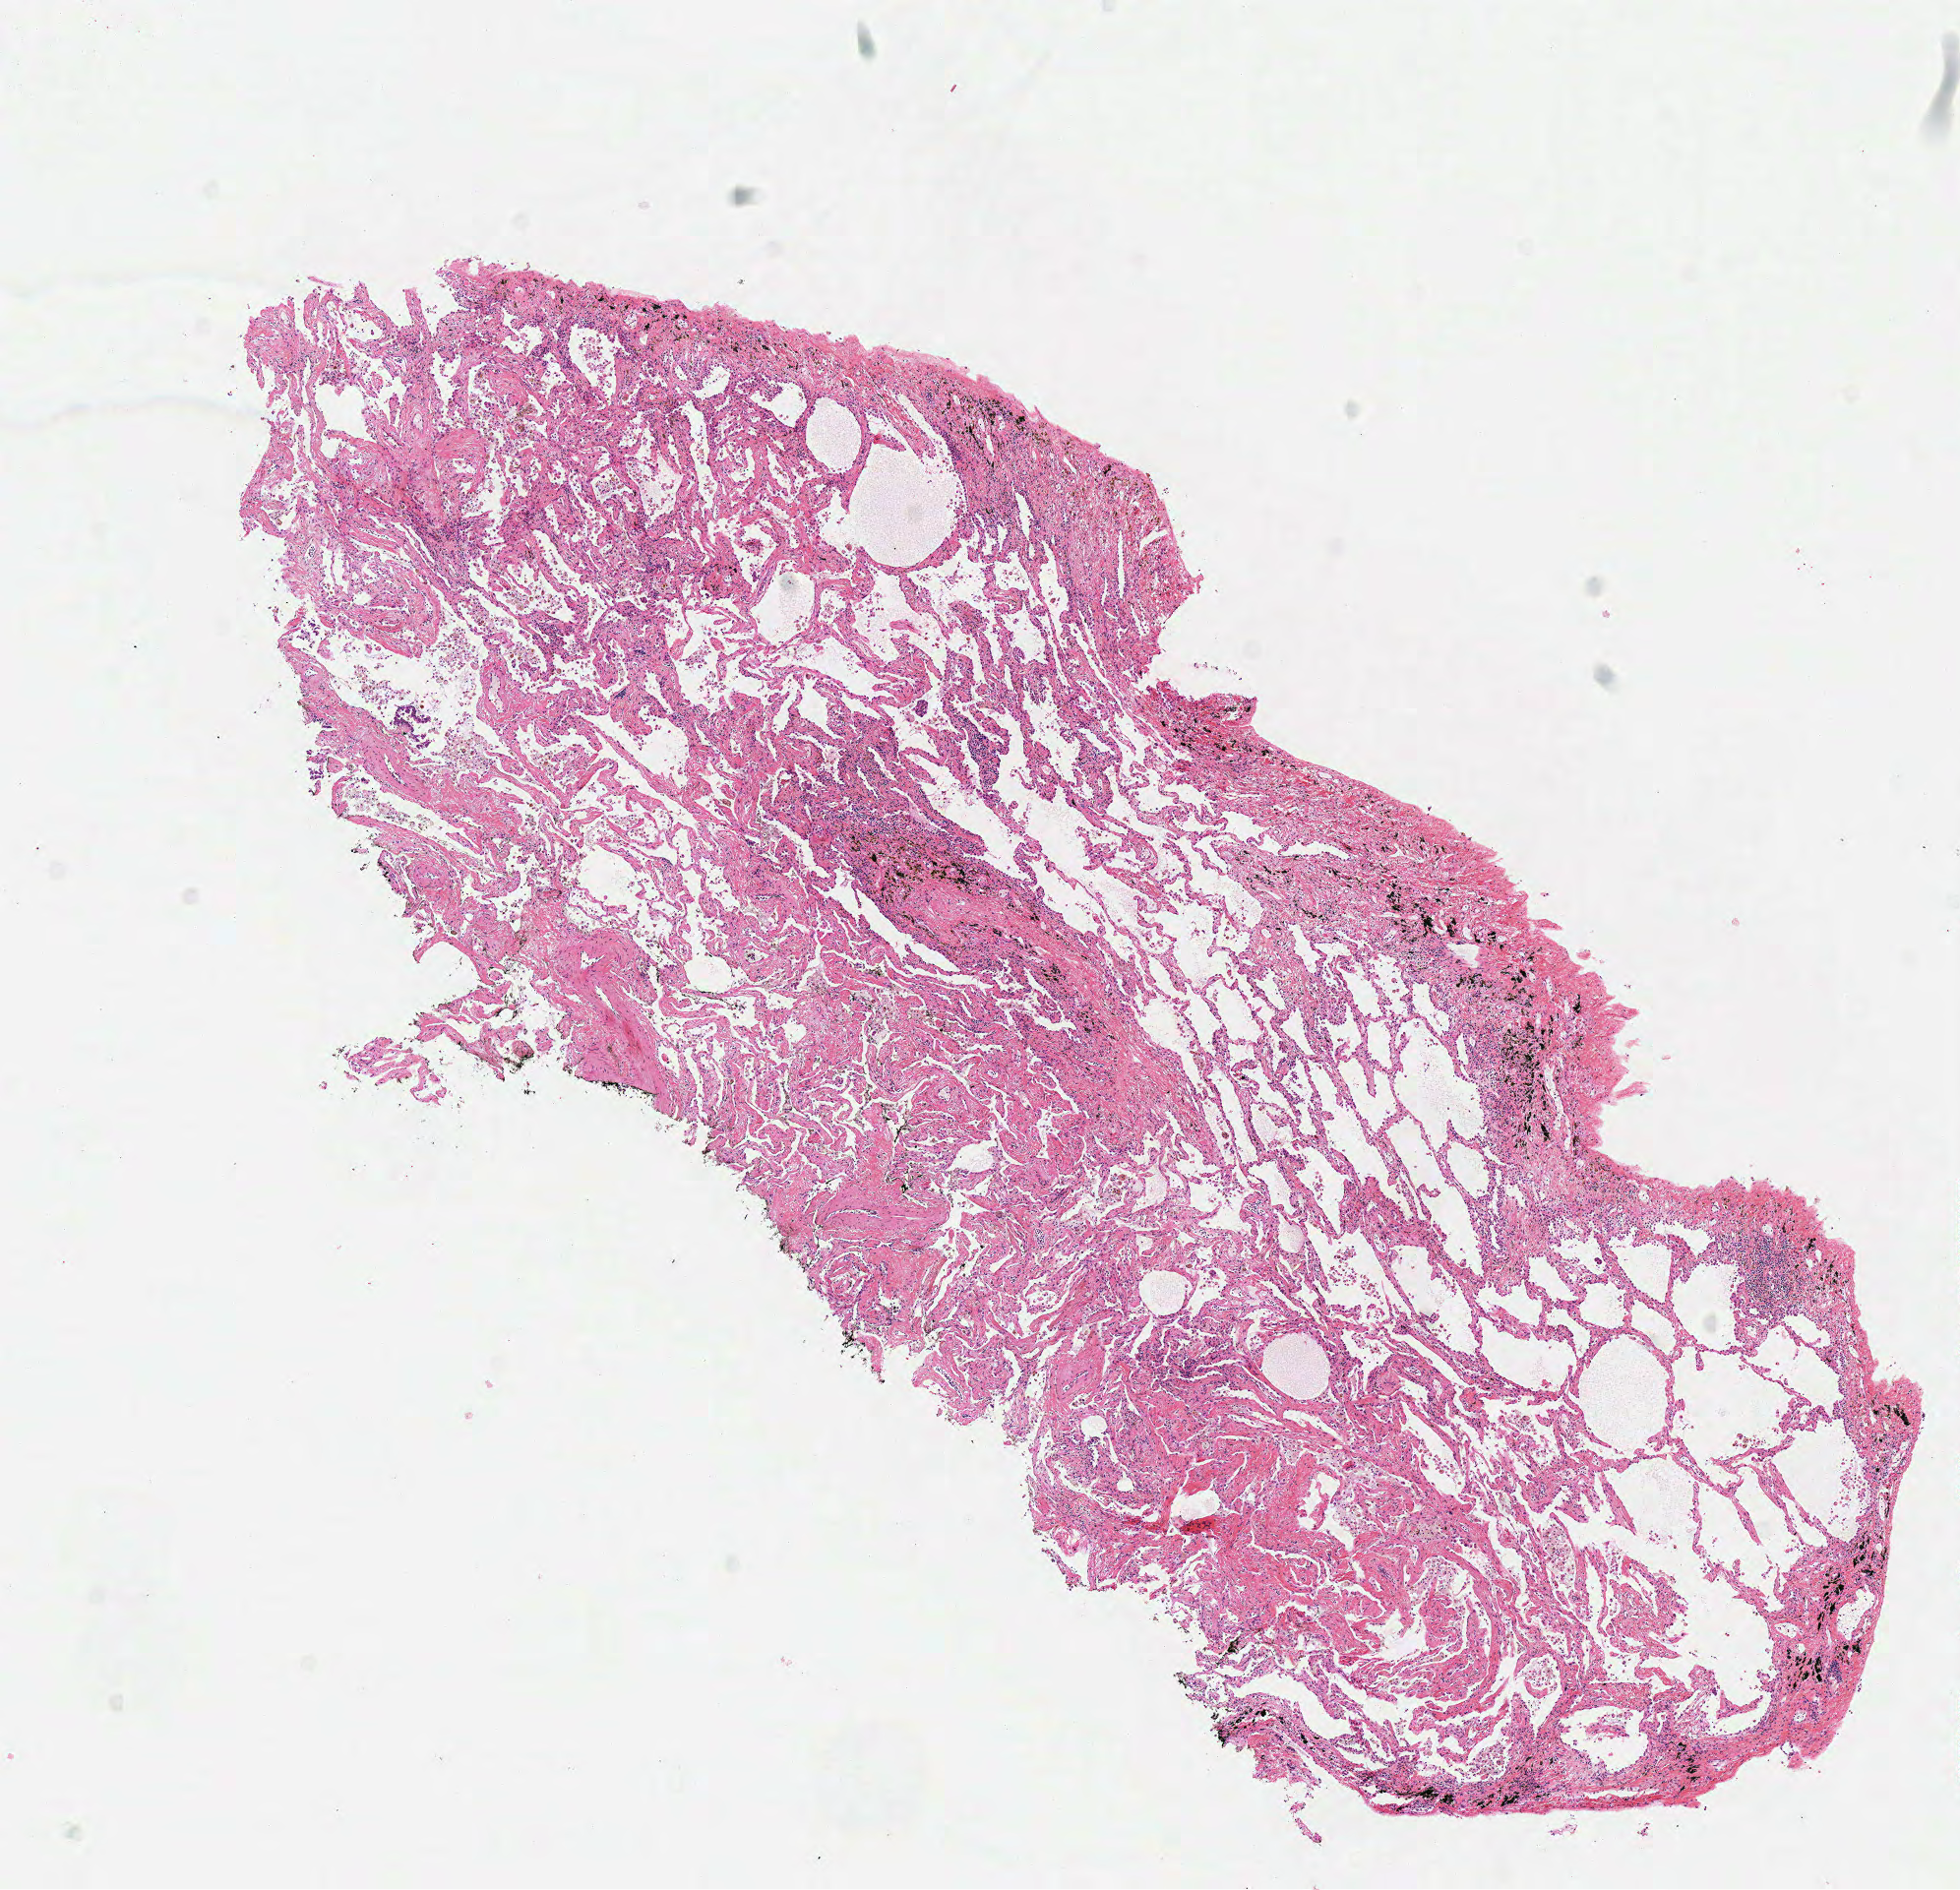
H&E-stained whole-slide image, whole scanned area (about 7.8 x 7.6 mm, slide scanned at 40x) shown as a low-resolution overview; frozen section from the top of the tissue portion; sample: solid tissue normal (non-tumour tissue), lung. Male, age 77 years at initial diagnosis.
* this section: solid tissue normal (non-tumour) sample from the same patient
* patient diagnosis: Papillary adenocarcinoma, NOS